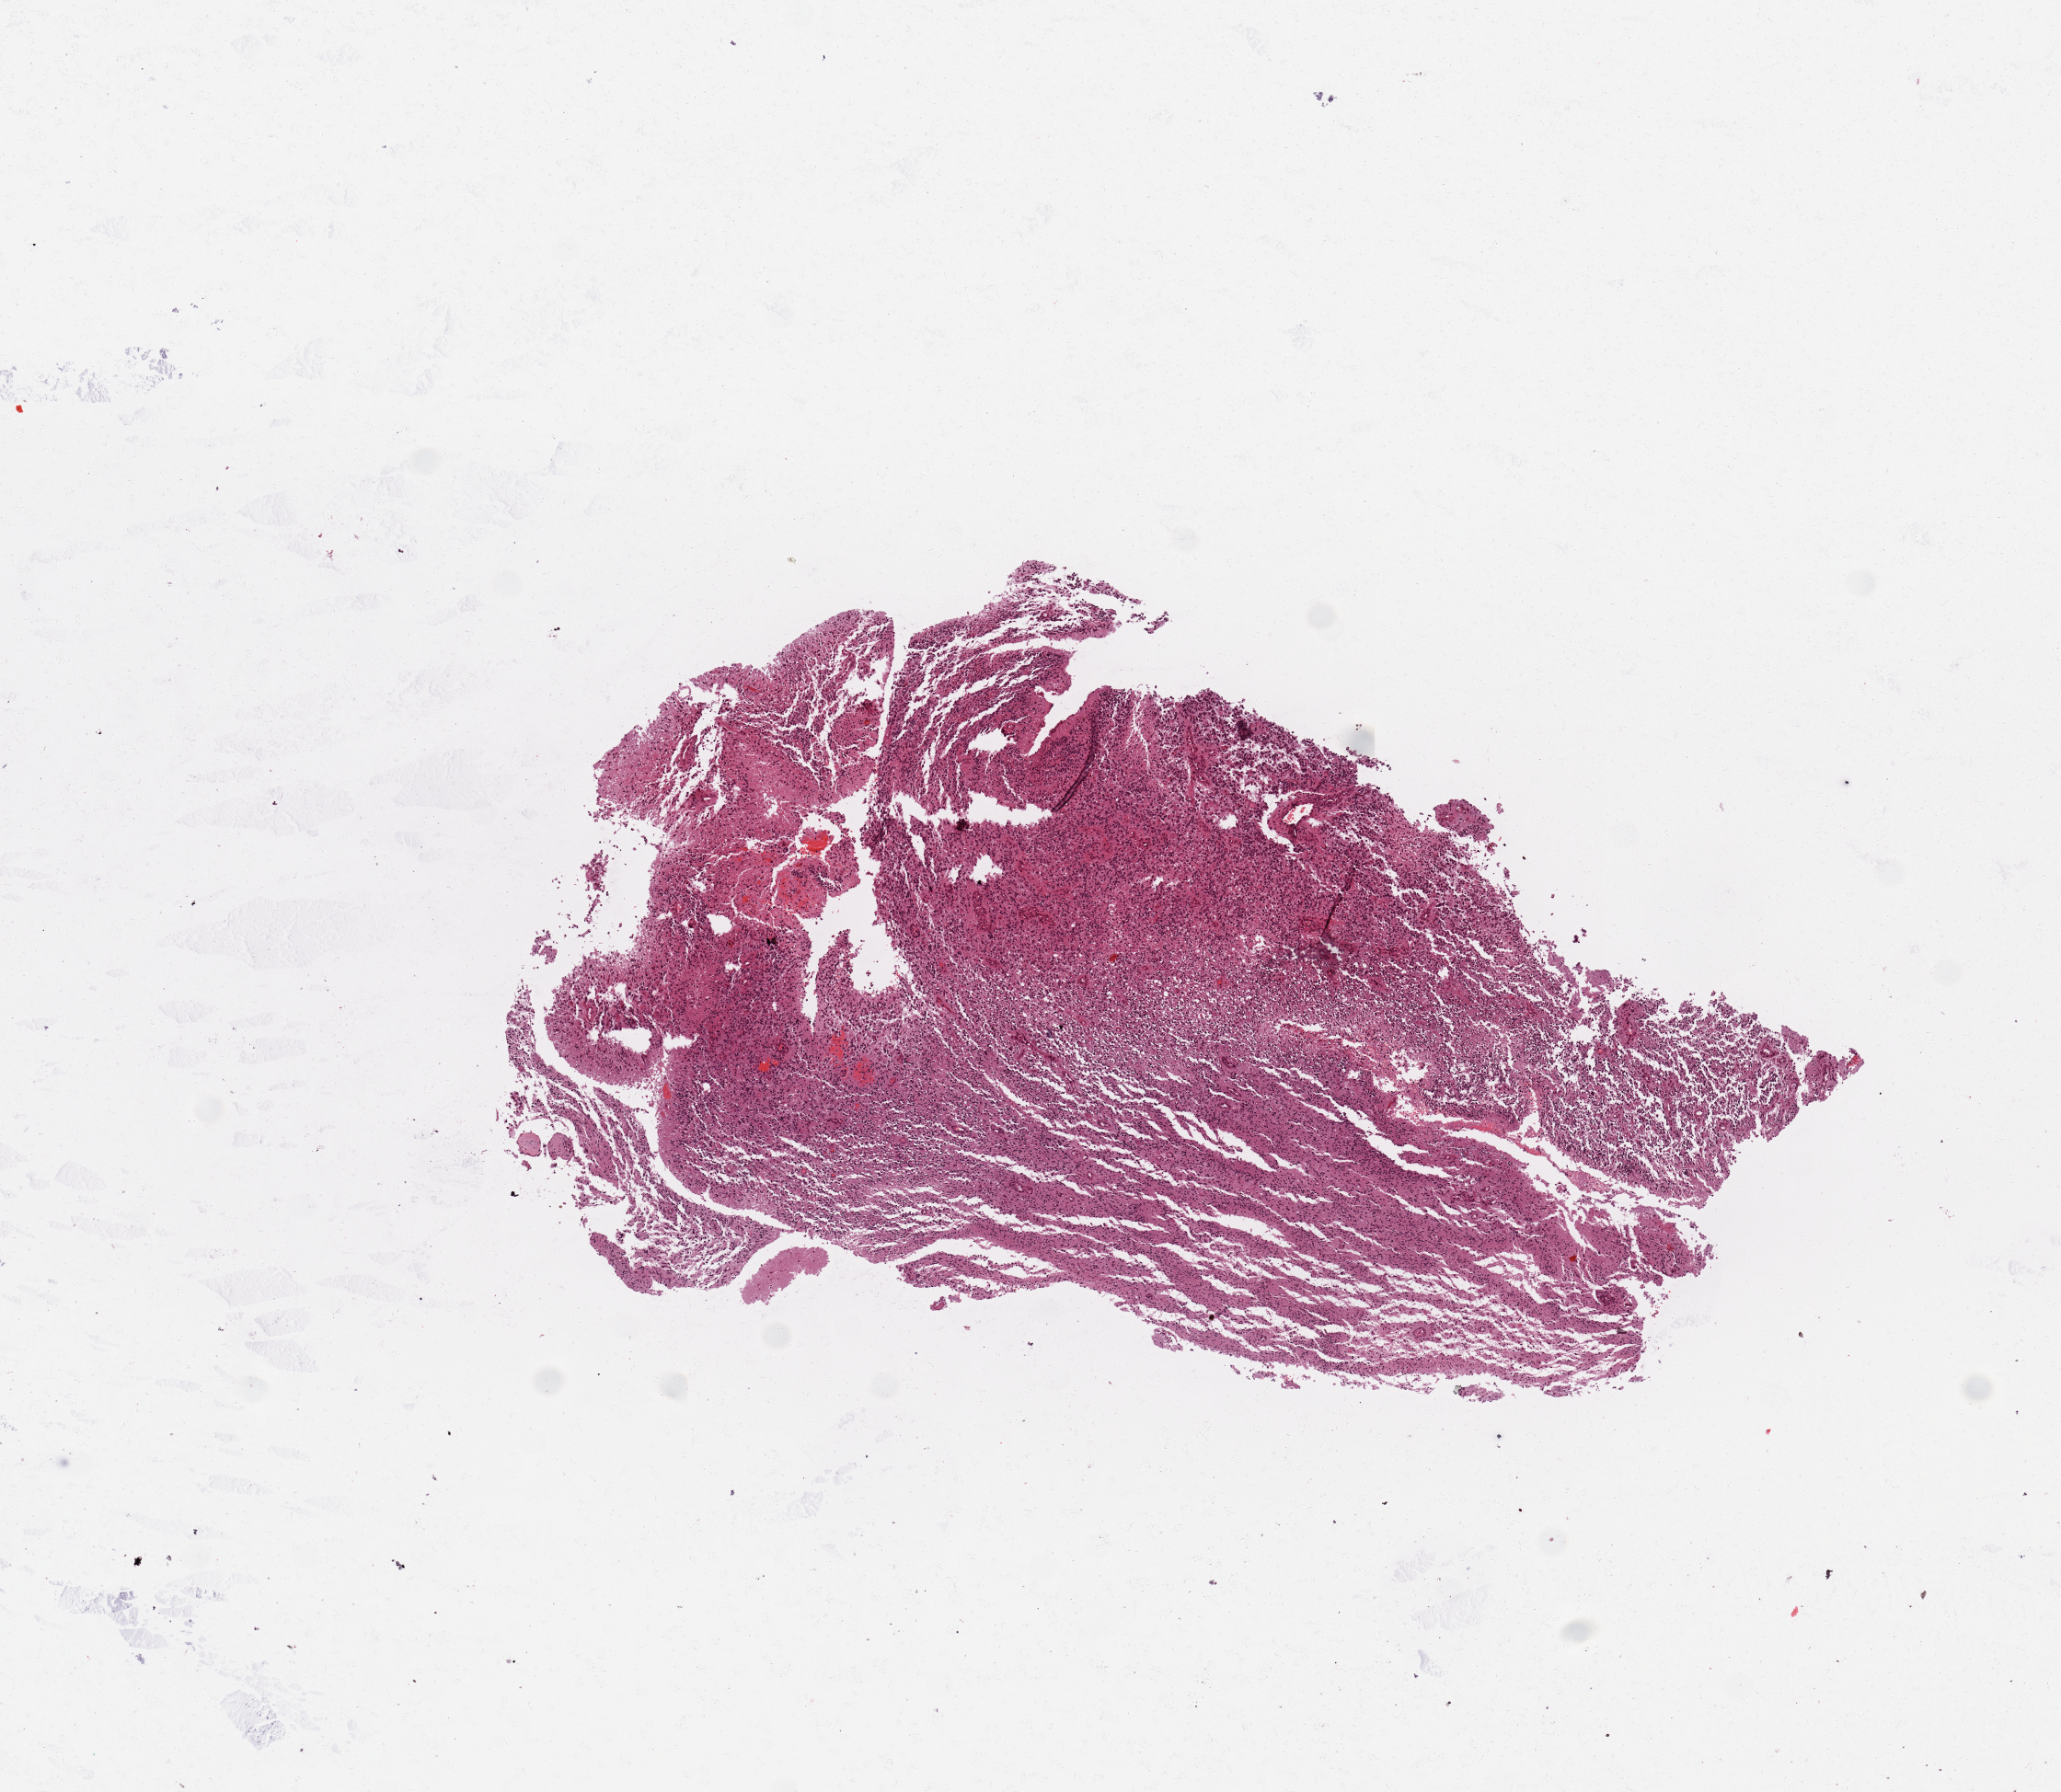
H&E whole-slide image — whole scanned area (about 8.9 x 7.7 mm, from a 20x scan) shown as a low-resolution overview; tumour tissue sample, sampled site: brain. Patient: female, age 48 years. Pathologist review of this section (percent, as recorded): tumour nuclei 90%, necrosis 3%.
Histologic diagnosis: Glioblastoma.